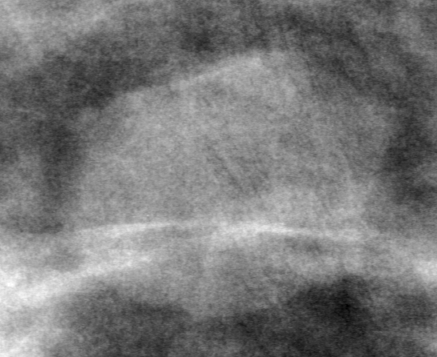
Crop from a digitized film mammogram around one marked abnormality, right breast, CC view, BI-RADS breast density category 2 (scale 1–4).
Marked abnormality: mass, shape oval, margins circumscribed; BI-RADS assessment category 3; subtlety rating 3 on a 1 (subtle) to 5 (obvious) scale; pathology (as recorded): benign.